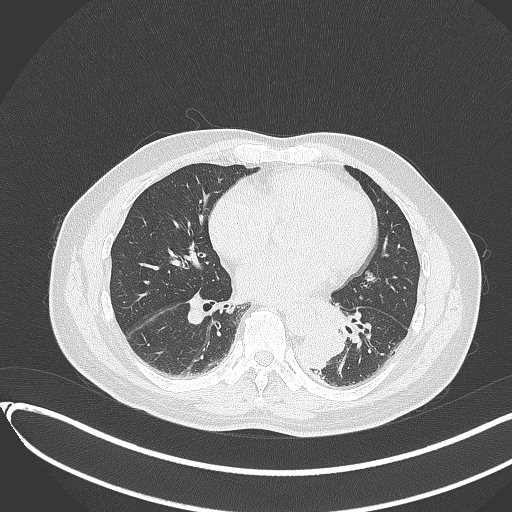
Chest CT, one axial slice; slice 142 of 417 in the series (ordered by position); reconstruction kernel B70f; 120 kVp; lung window (W 1500 / L -600 HU); 512 × 512 image matrix, field of view 400 × 400 mm. Male patient, age 54 years. Case-level facts recorded for this patient, not image findings: clinical TNM (as recorded): T3 N0 M0.
Structures marked on this image (rectangle marked by the reading radiologist):
- lung tumour (recorded histology: squamous cell carcinoma): bounding box (x1, y1, x2, y2) in pixels: (295, 321, 348, 372)